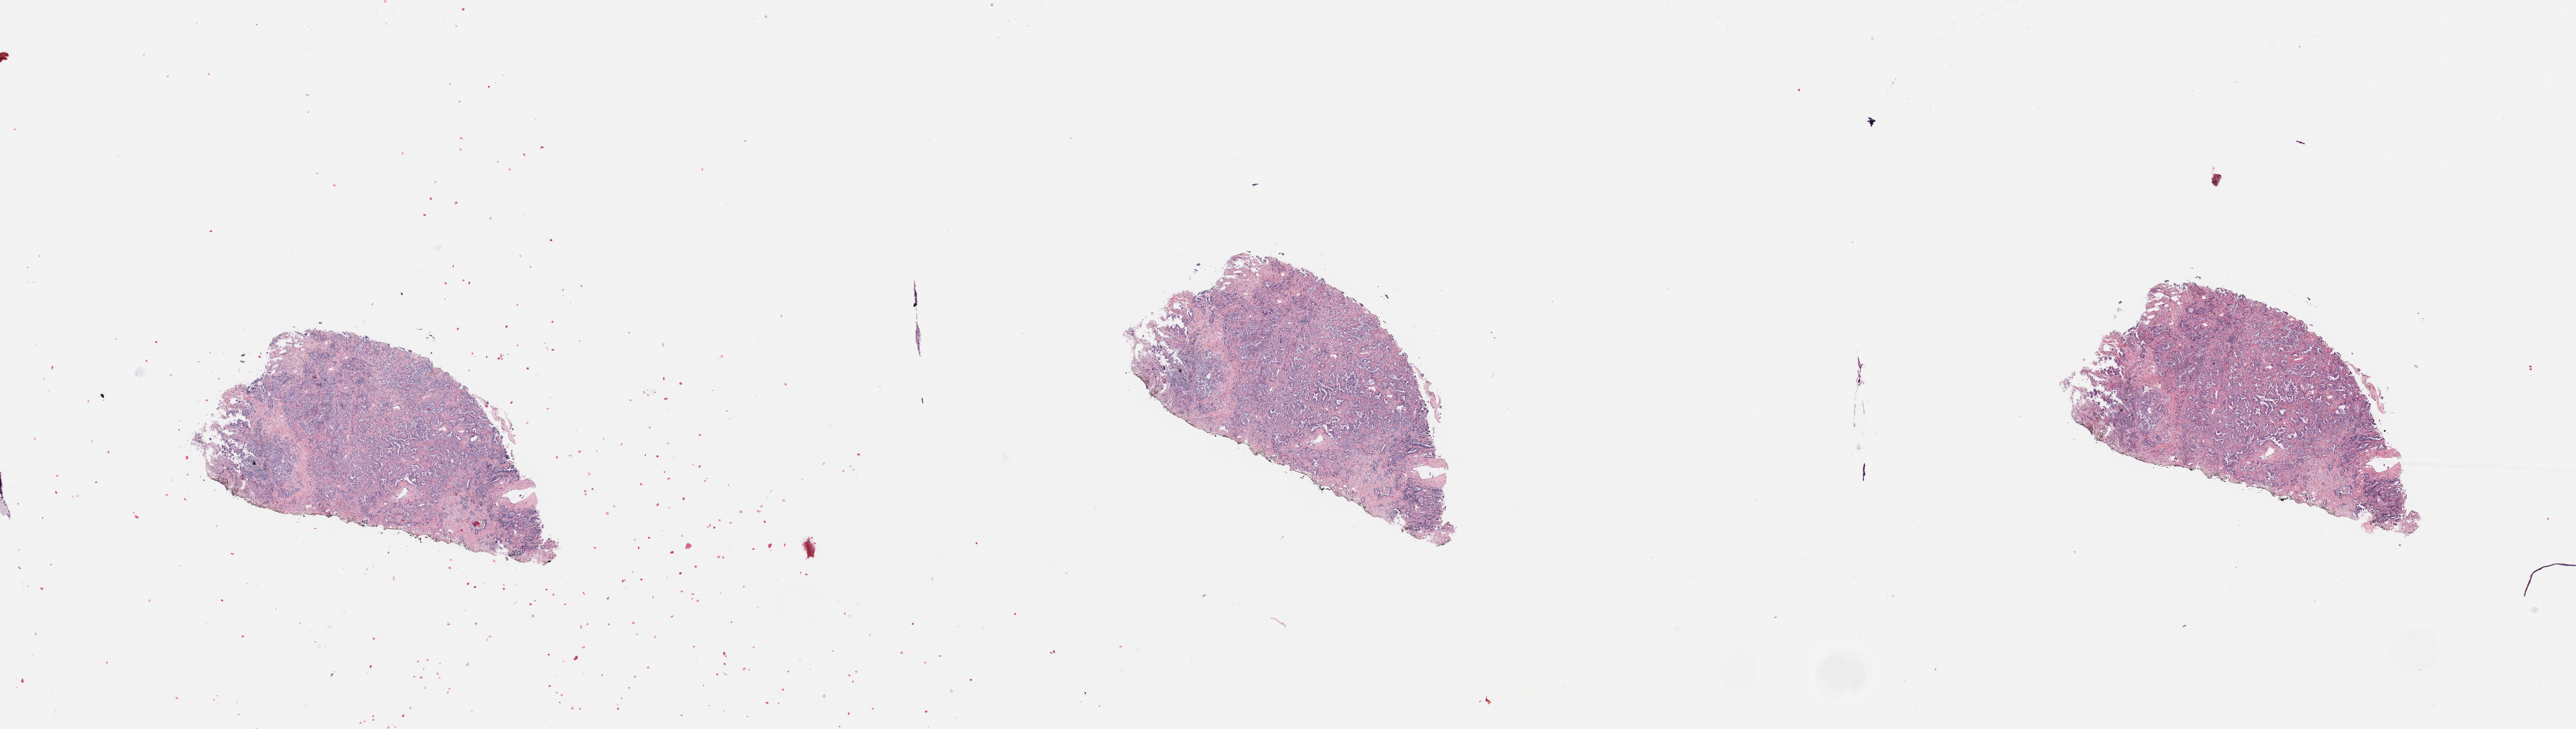
Whole-slide histology image, Hematoxylin and eosin (H&E) stained, shown as a low-resolution overview of the whole scanned area (about 31.5 x 8.9 mm, slide scanned at 20x). Tumour tissue sample, sampled site: lung. 68-year-old female patient. Histologic grade: G2 (moderately differentiated). Pathologist review of this section (percent, as recorded): tumour nuclei 70%, necrosis 5%.
- AJCC pathologic stage: IB
- primary tumour site (as recorded): right upper lobe
- diagnosis: Adenocarcinoma, NOS